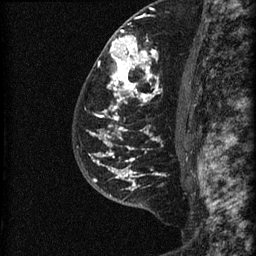
Breast MRI (dynamic contrast-enhanced), one sagittal slice; slice 44 of 60 in the series (ordered by position); dynamic contrast-enhanced series, image 2 of 3 at this slice position (ordered by acquisition); 1.5 T; TE 4.2 ms, TR 22.7 ms; 1.5 mm slice thickness; 256 × 256 image matrix, field of view 180 × 180 mm. Patient: female, 48 years. Case-level facts recorded for this patient, not image findings: setting: breast cancer imaged before/during neoadjuvant chemotherapy; receptor status: triple-negative.
Structures marked on this image (semi-automatic segmentation, software-assisted and operator-edited):
- analysis volume of interest (the breast-tissue region the enhancement analysis was run in; not a lesion): bounding box [x1, y1, x2, y2] px = [81, 23, 186, 202]
- tumour enhancement mask (voxels above the 90 % enhancement threshold inside the analysis volume of interest): [90, 30, 165, 190]